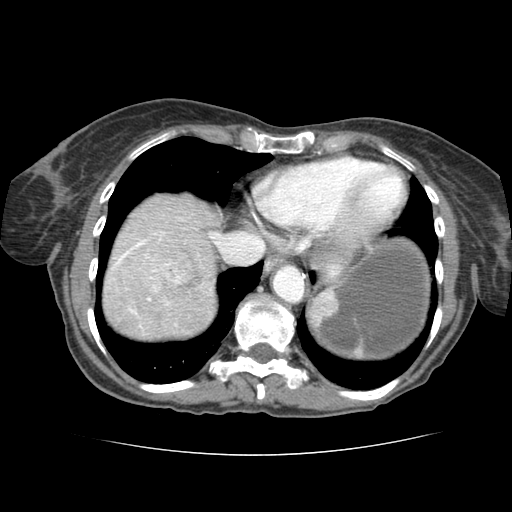
Contrast-enhanced abdominal CT (liver protocol), one axial slice; position 71 of 77 along the scan axis; 120 kVp; soft-tissue window (W 400 / L 40 HU); 2.5 mm slice thickness; 512 × 512 image matrix, field of view 340 × 340 mm. From the clinical record (not read from this slice): diagnosis: hepatocellular carcinoma (patient treated with transarterial chemoembolisation; whether this scan precedes or follows treatment is not stated here); TNM stage (as recorded): Stage-I; Child-Pugh class: A; tumour differentiation: well differentiated; tumour nodularity: uninodular.
Outlined on this slice (semi-automatically segmented with operator editing):
- abdominal aorta: bounding box [x1, y1, x2, y2] px = [273, 265, 305, 302]
- liver parenchyma outside the tumour (the mass and vessels are separate outlines, so this box may not span the whole liver): [108, 200, 222, 323]